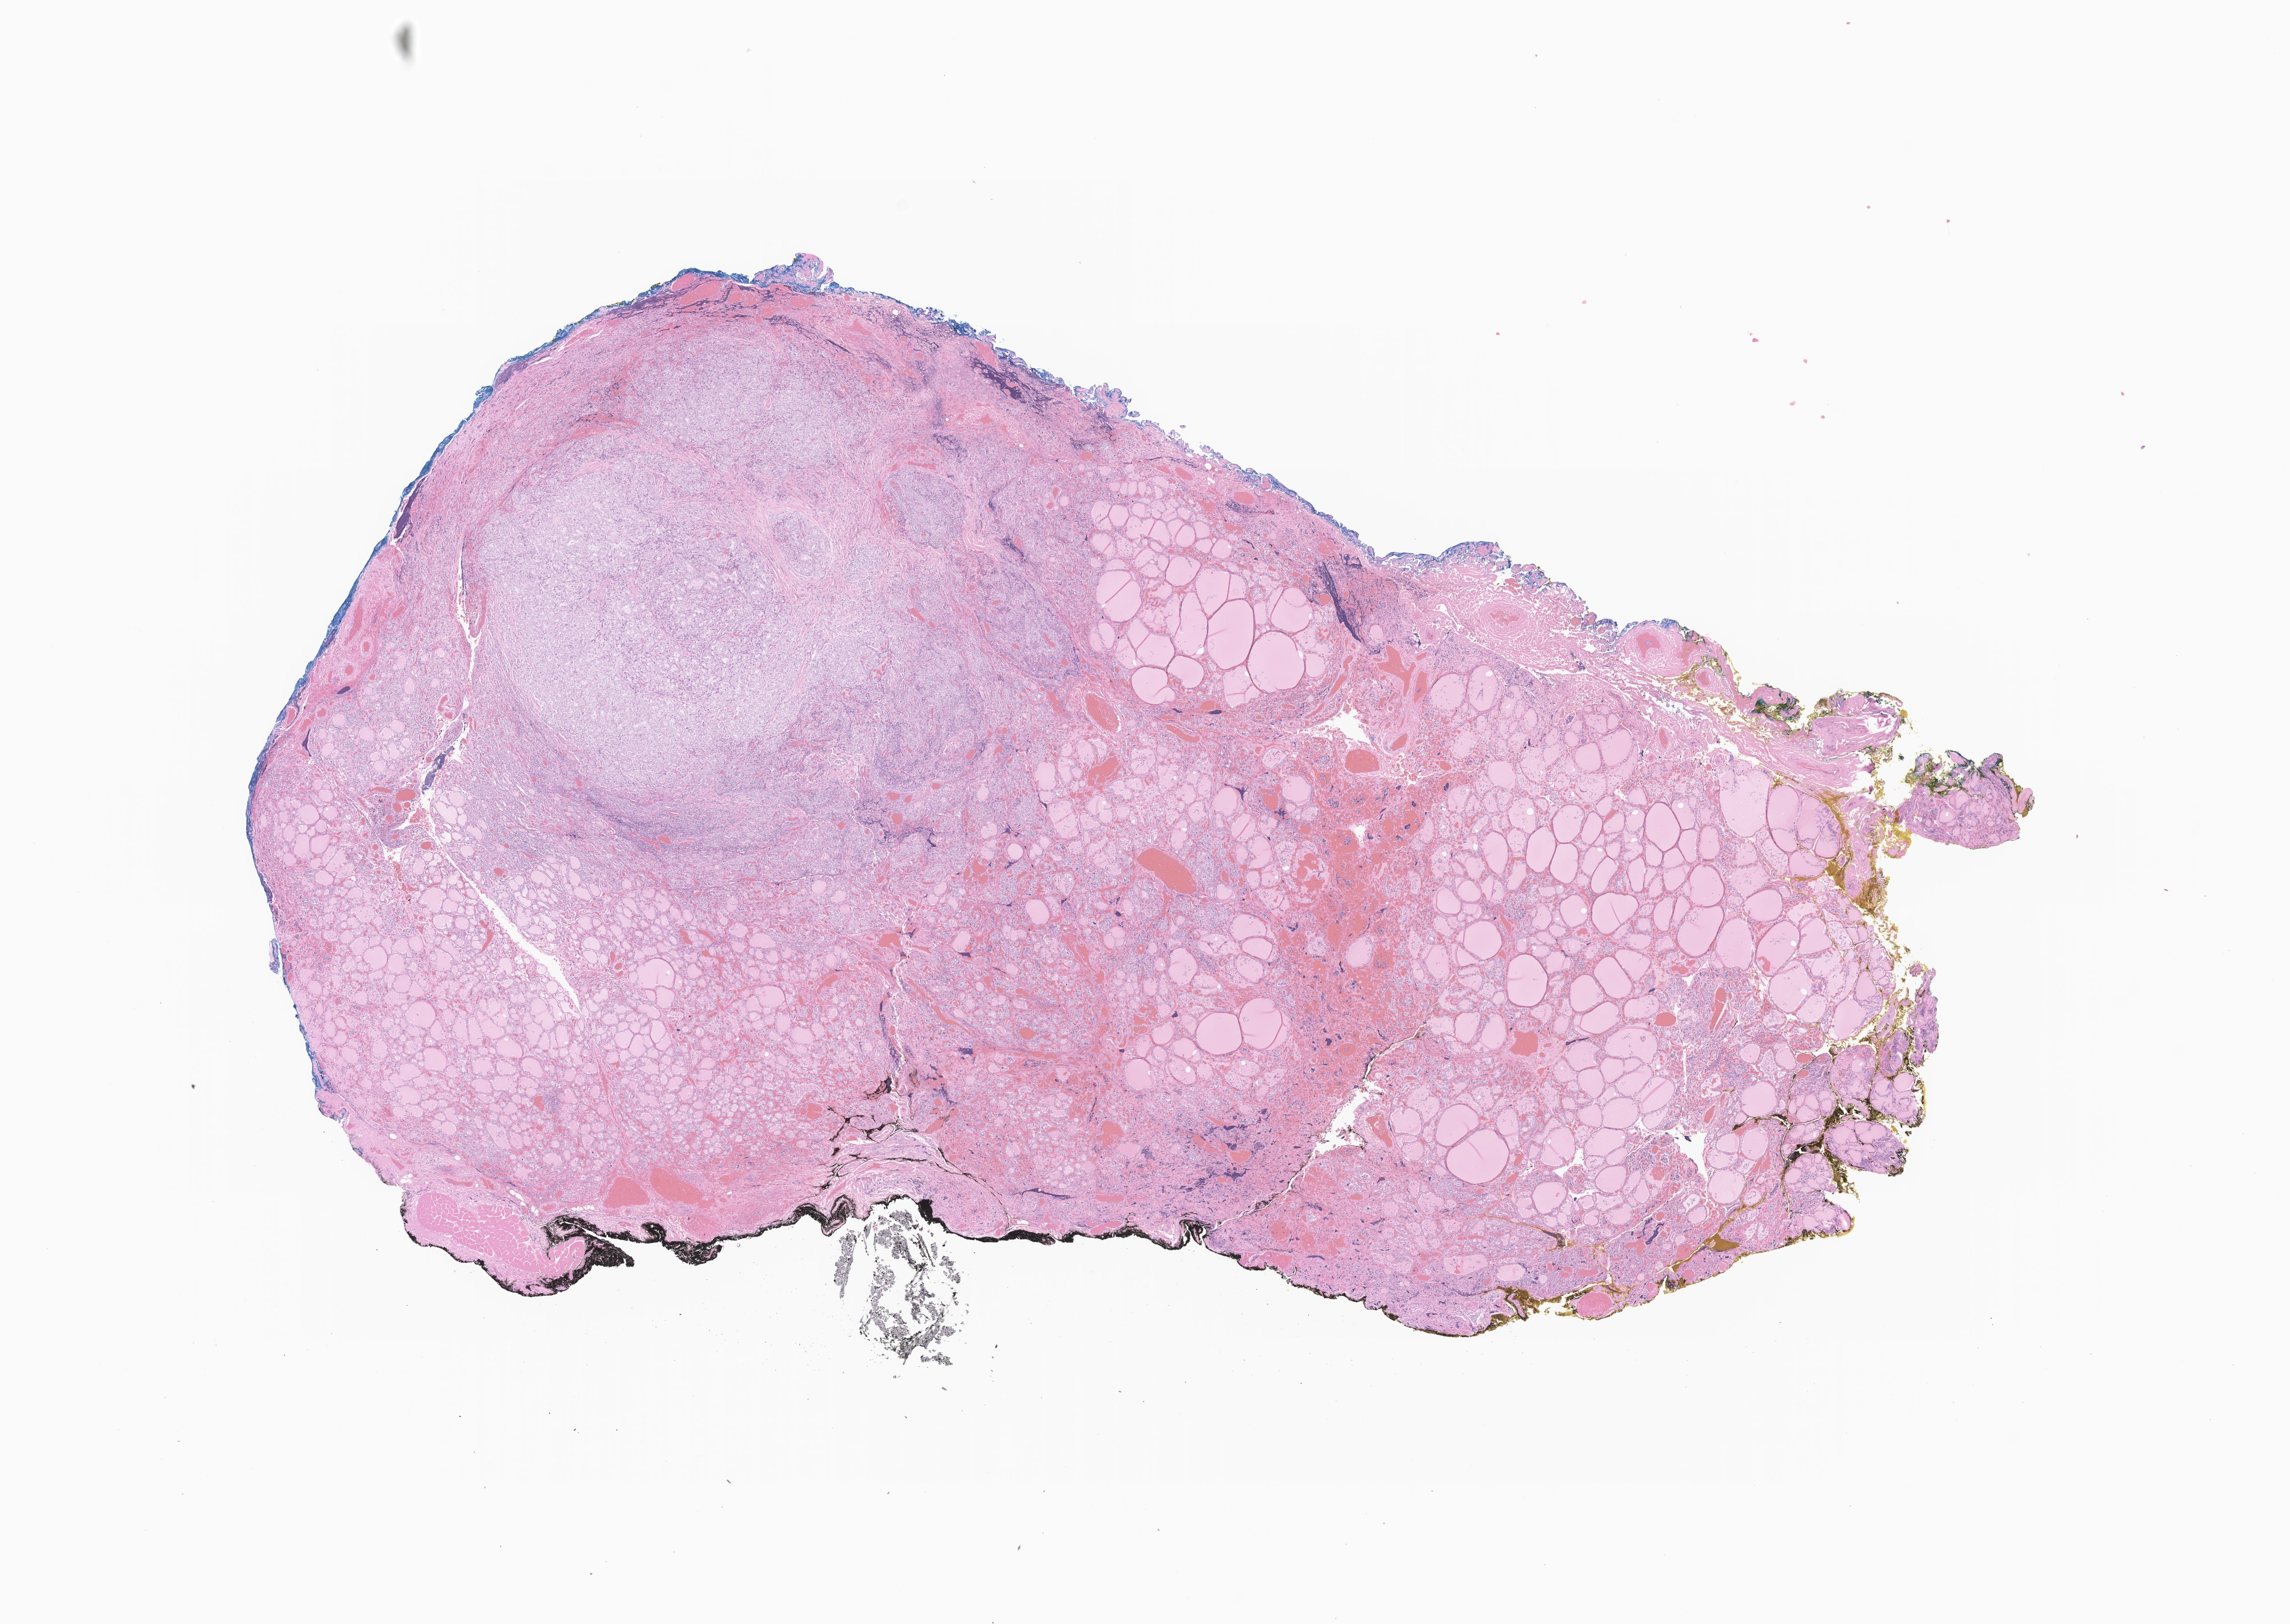
Hematoxylin and eosin (H&E) whole-slide image of tumor tissue from the thyroid, shown as a low-resolution overview of the whole scanned area (about 16.9 x 12.0 mm), FFPE section. Patient female; age 250 months (20 years 10 months).
• diagnosis (ICD-O-3 morphology term): Carcinoma, NOS